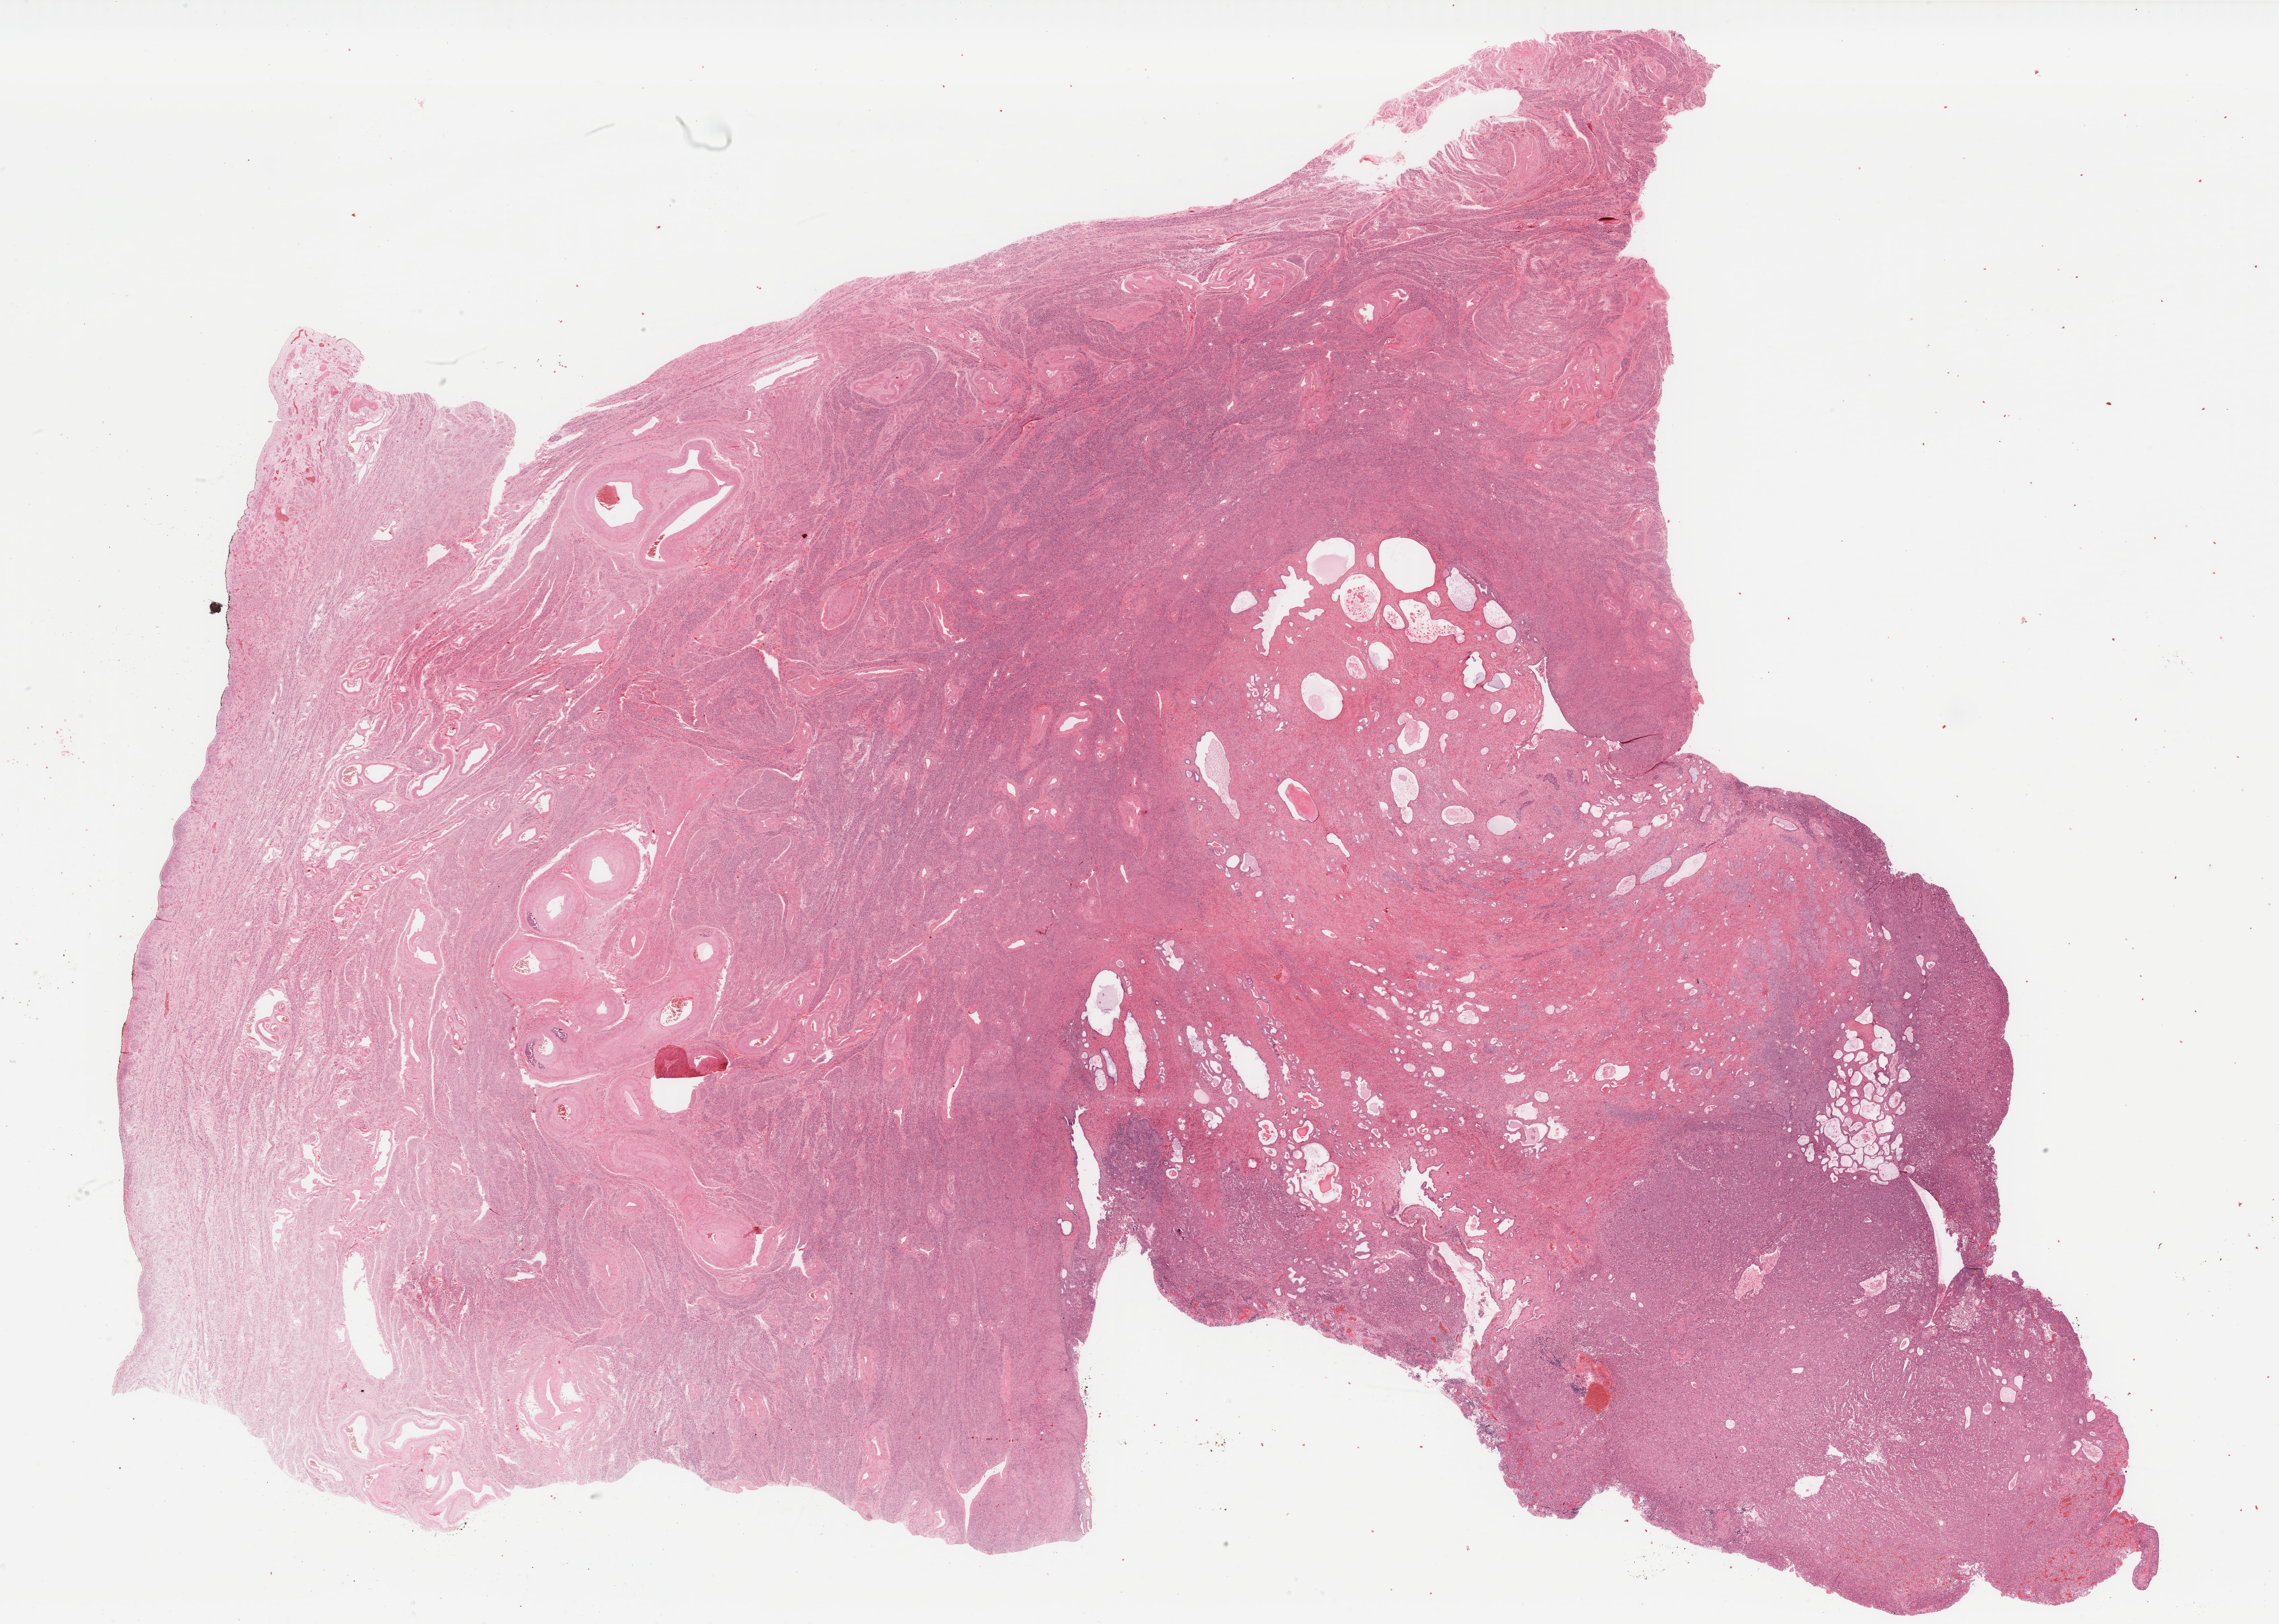
H&E whole-slide image, whole scanned area (about 31.9 x 22.7 mm, slide scanned at 40x) shown as a low-resolution overview, formalin-fixed paraffin-embedded (FFPE) diagnostic section, primary tumour sample from the uterus. Female patient; age at initial diagnosis 84 years. Histologic grade: G3 (poorly differentiated).
FIGO stage: IA. Diagnosis: Serous cystadenocarcinoma, NOS (endometrium).